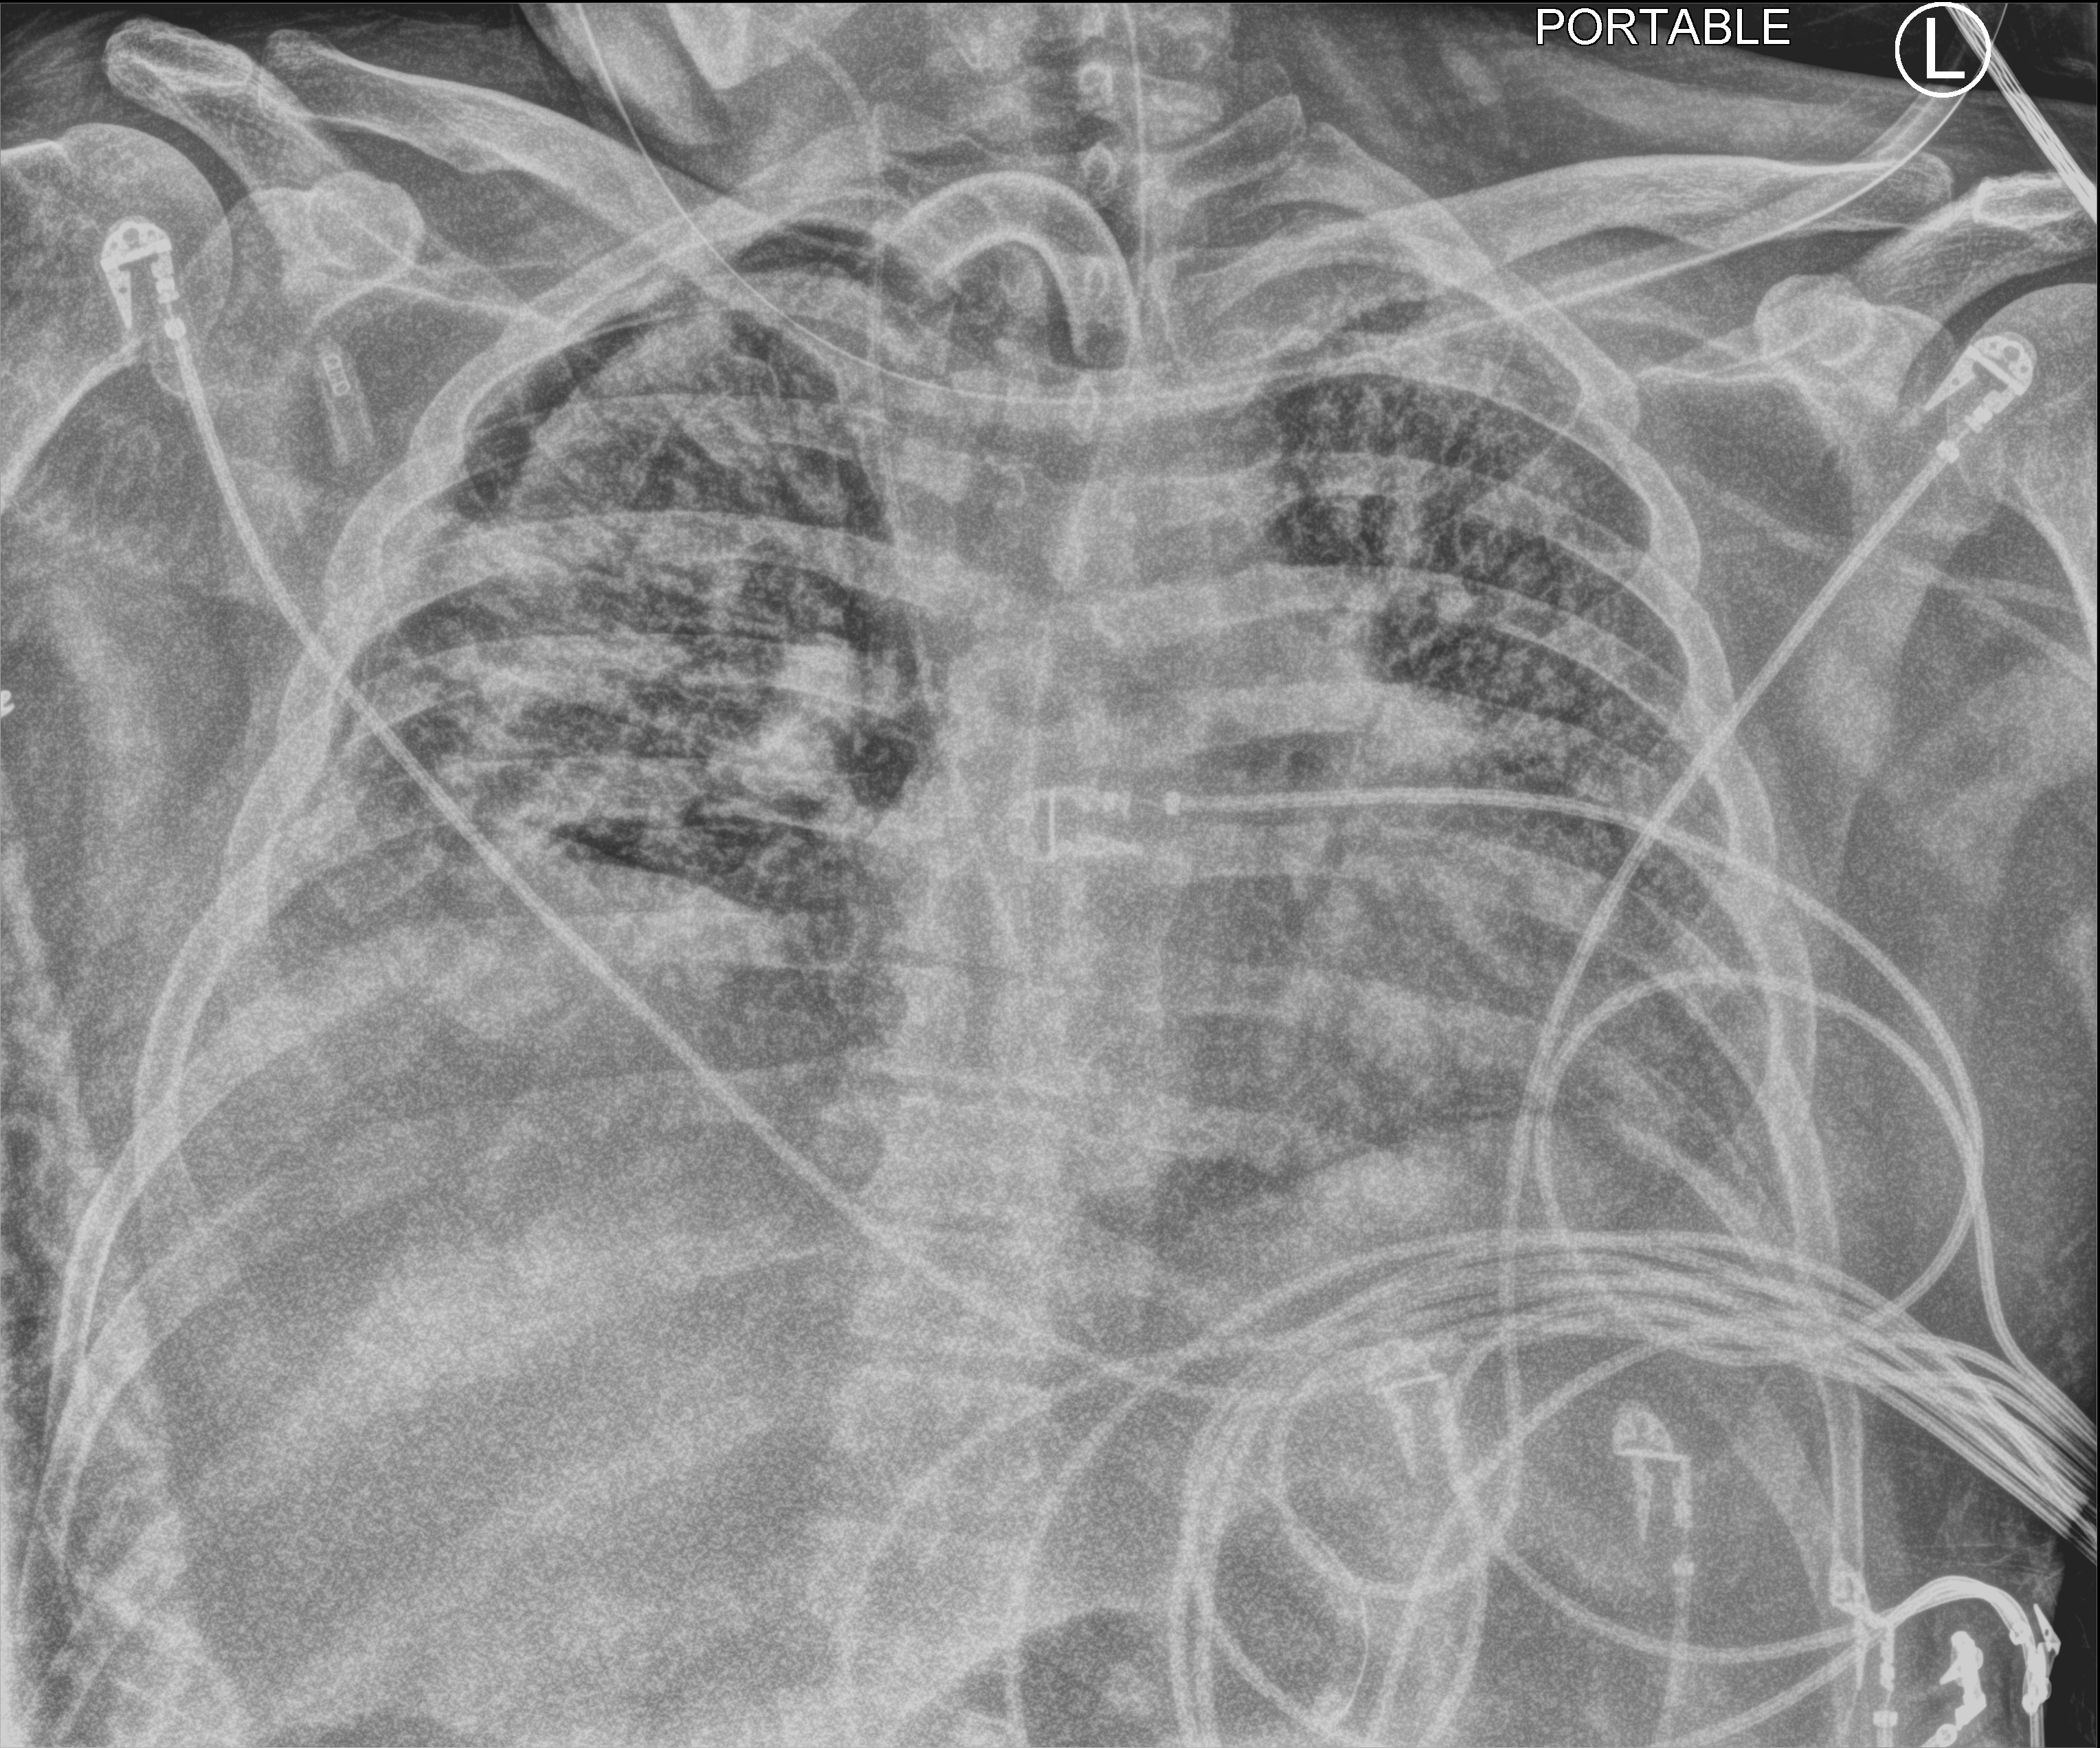
Portable chest radiograph; anteroposterior (AP) projection. Patient hospitalised with COVID-19; male, aged 18–59 years.
Admission-level facts for this patient (not findings on this image; timing relative to this image not recorded): mechanically ventilated during this hospital stay: yes; diabetes (admission record): no.